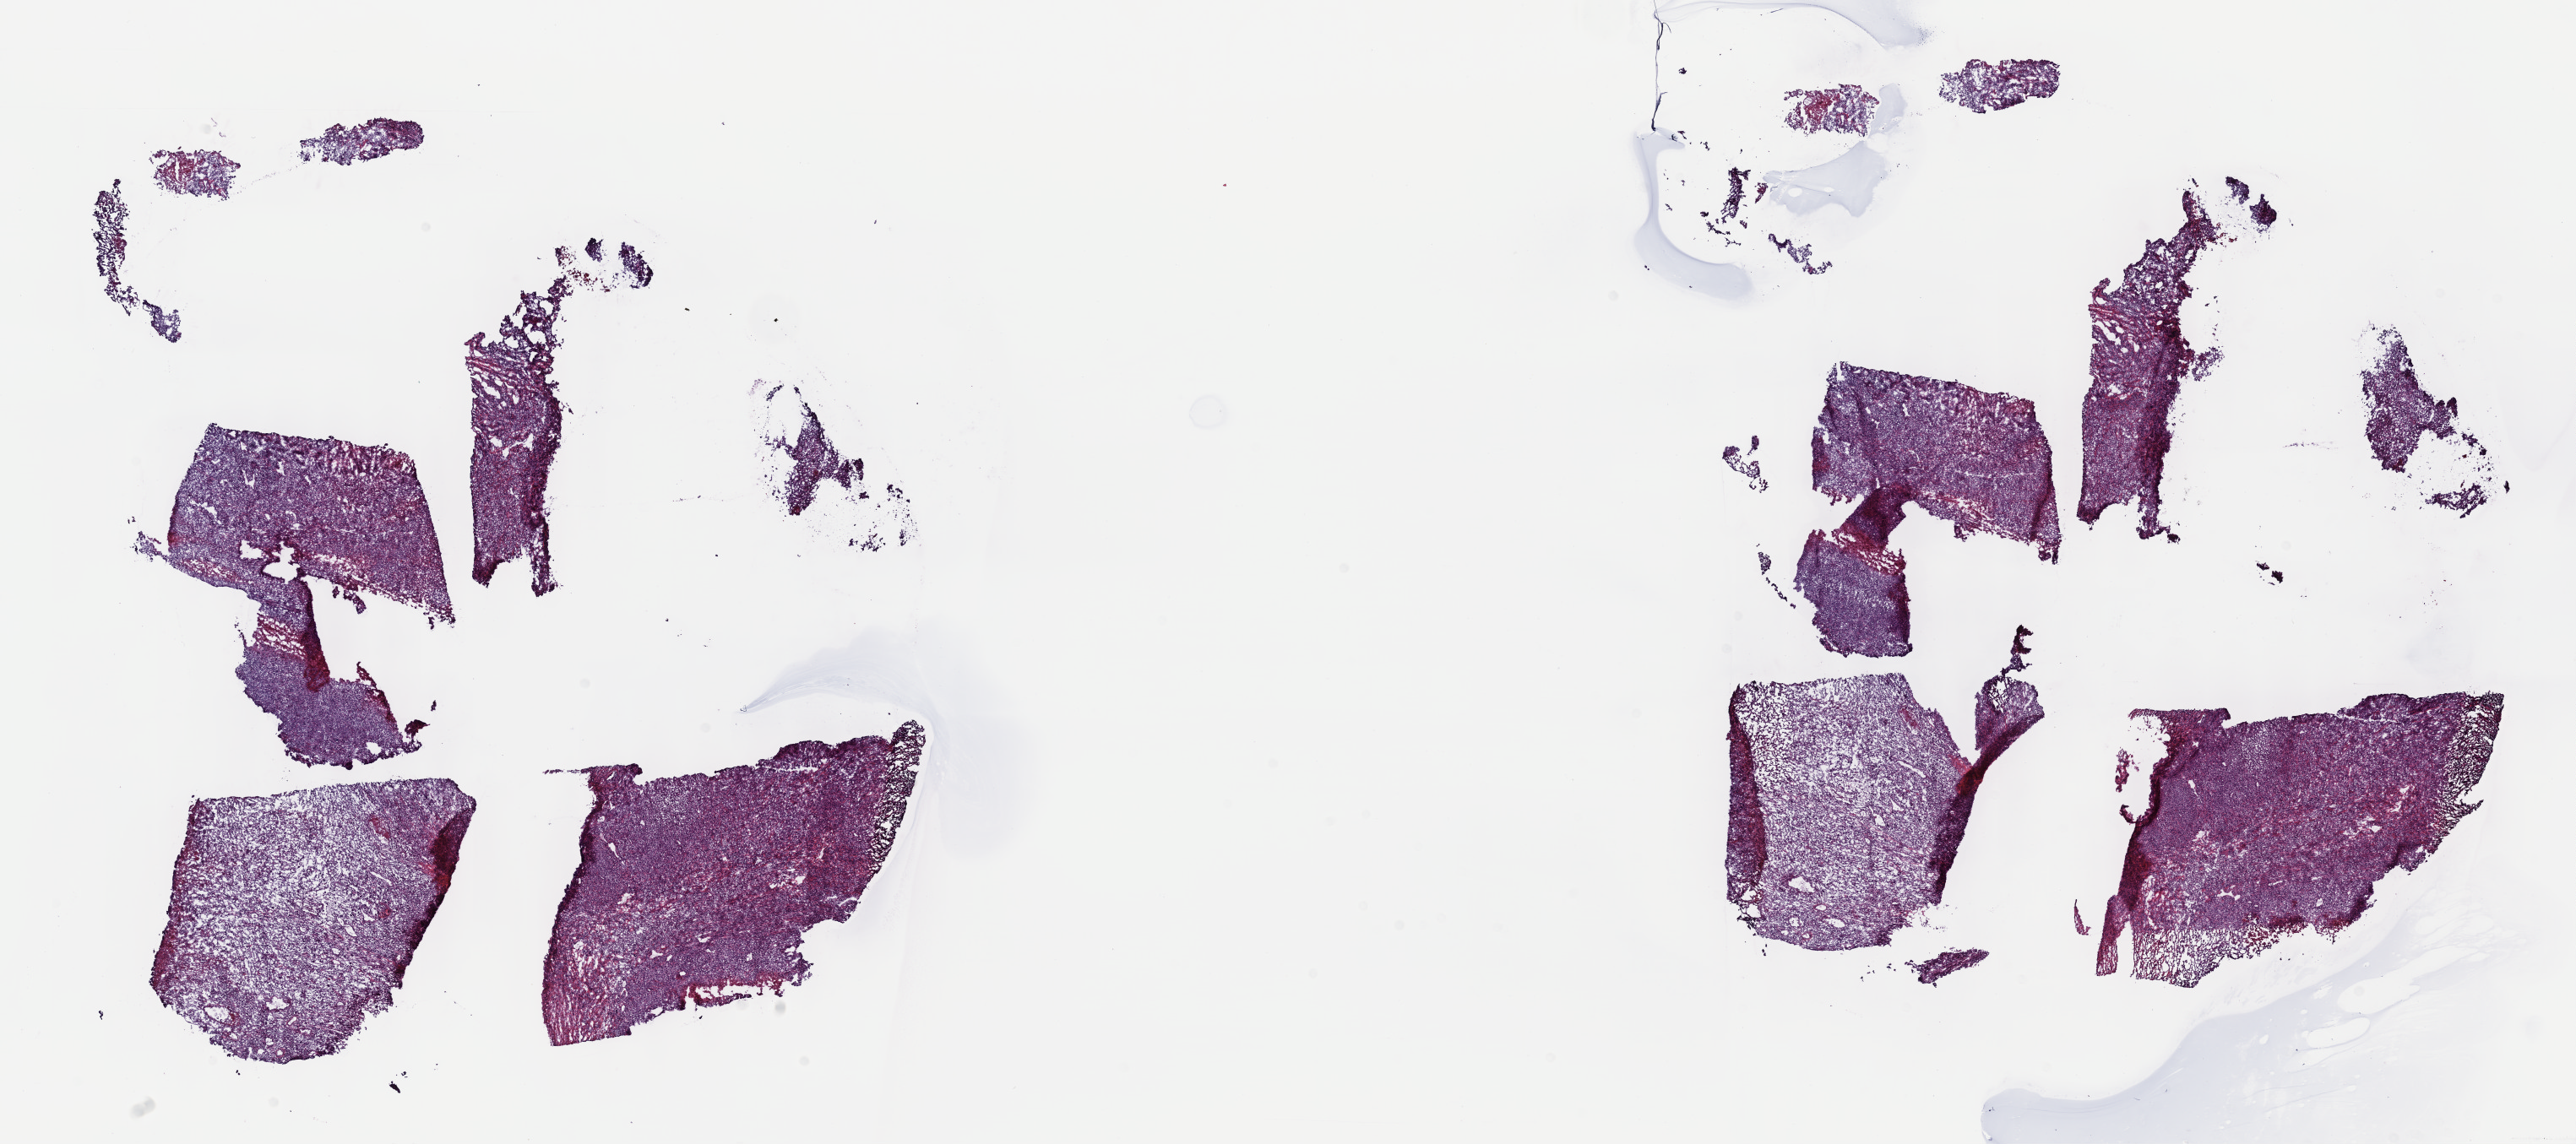
Digitized H&E tissue section (whole slide), a low-resolution overview of the entire scanned area, about 24.7 x 11.0 mm (acquisition: 40x scan), frozen section from the top of the tissue portion, other and unspecified parts of tongue, primary tumour sample. Male, age 53 years at initial diagnosis. Composition of this section per pathologist review: tumour cells 100%, tumour nuclei 80%, normal cells 0%, stromal cells 0%, necrosis 0%. Infiltration values recorded for this section: lymphocyte infiltration 1%, monocyte infiltration 0%, neutrophil infiltration 0%.
- diagnosis: Leiomyosarcoma, NOS (tongue, NOS)